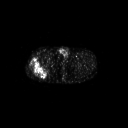
FDG PET of an extremity soft-tissue mass (from a PET/CT study), one axial slice. Position 266 of 267 along the scan axis. 3.27 mm slice thickness. 128 × 128 image matrix, field of view 700 × 700 mm. Patient: male, 43 years. From the clinical record (not read from this slice): histological type: poorly differentiated synovial sarcoma; grade: high; site of the primary tumour: right buttock.
Structures marked on this image (expert contour drawn on MRI and transferred to this co-registered scan by the dataset authors):
- gross tumour volume including surrounding oedema: bounding box (x1, y1, x2, y2) in pixels: (29, 58, 51, 78)
- gross tumour volume (mass): (29, 58, 48, 78)